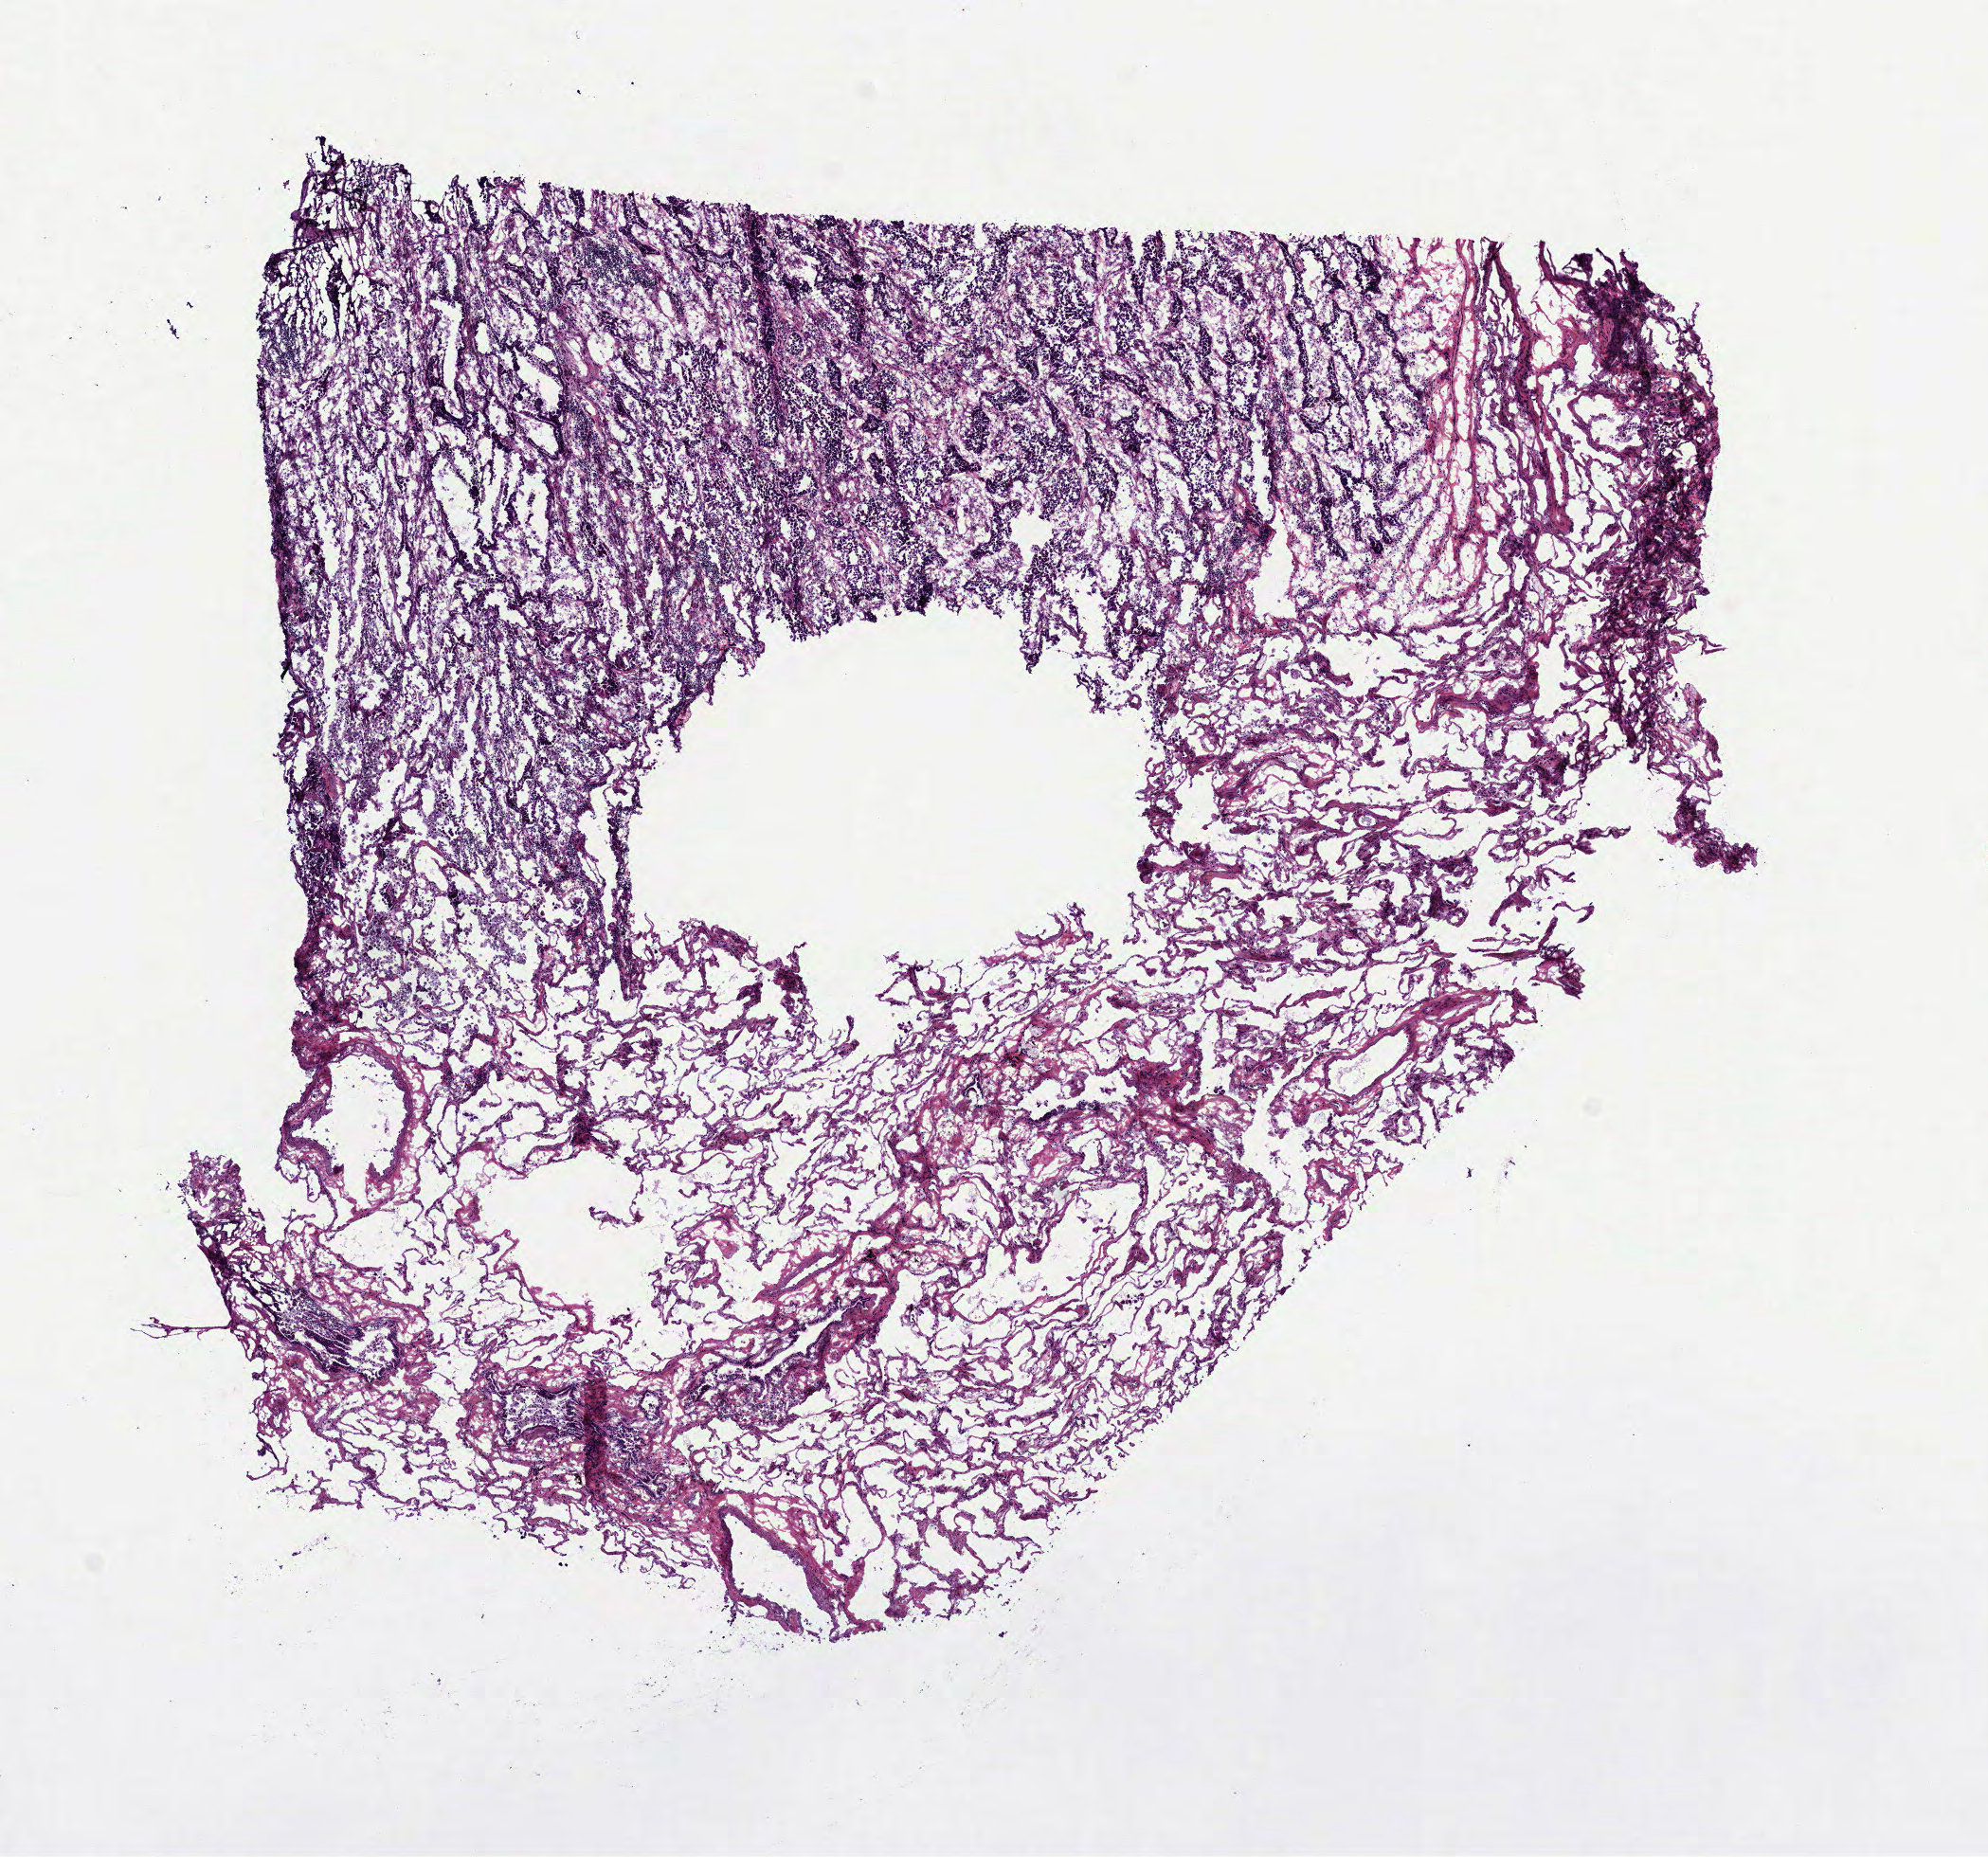
Whole-slide histology image, H&E-stained — low-resolution overview of the scanned area, about 8.5 x 7.9 mm; frozen section from the bottom of the tissue portion; primary tumour sample from the lung. Patient: female, age at initial diagnosis 76 years. Composition of this section per pathologist review: tumour cells 40%, tumour nuclei 40%, normal cells 50%, stromal cells 10%, necrosis 0%.
TNM: T1 N1 M0. Pathologic diagnosis: Adenocarcinoma, NOS. AJCC pathologic stage: IIA (6th edition).